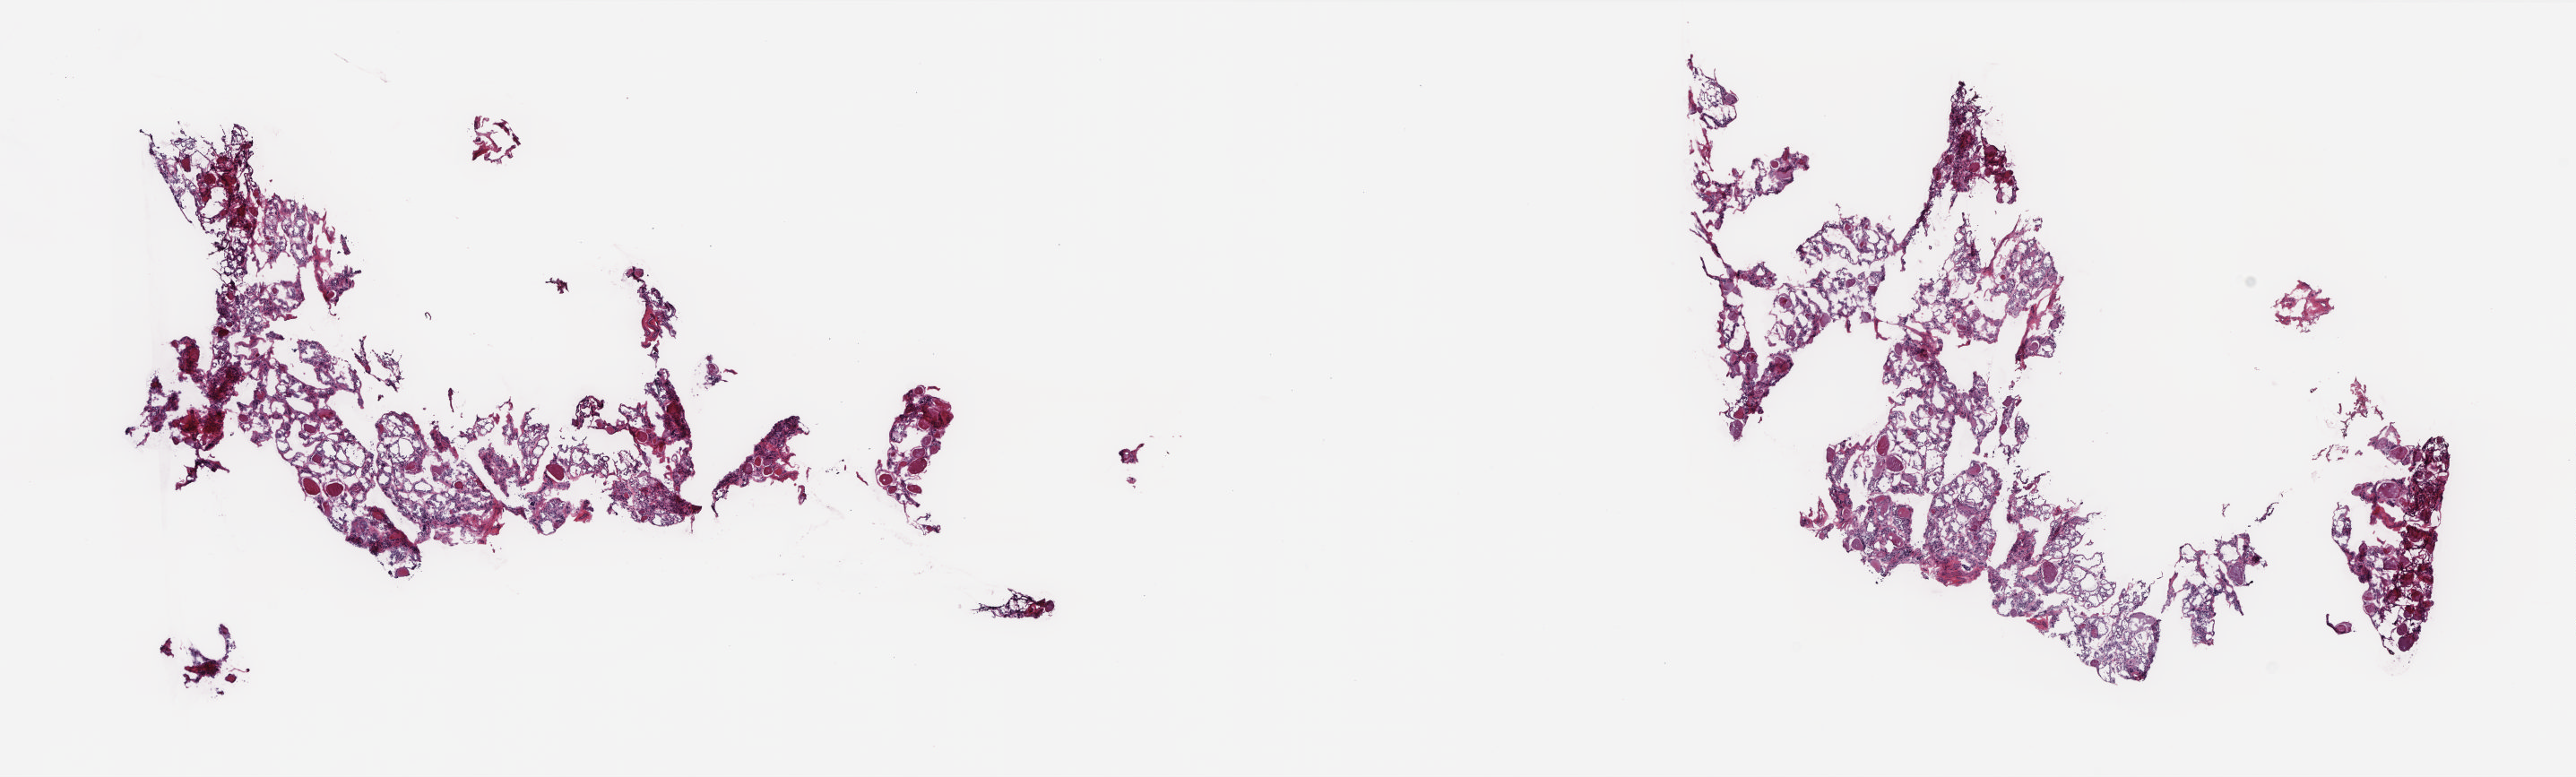
Whole-slide histology image, H&E, whole scanned area (about 23.0 x 6.9 mm, from a 20x scan) shown as a low-resolution overview, frozen section from the top of the tissue portion, sample: solid tissue normal (non-tumour tissue), thyroid. Patient: female, age at initial diagnosis 55 years. Pathologist review of this section (percent, as recorded): tumour cells 0%, tumour nuclei 0%, normal cells 100%, stromal cells 0%, necrosis 0%. Infiltration values recorded for this section: lymphocyte infiltration 4%, monocyte infiltration 1%, neutrophil infiltration 0%.
- this section: solid tissue normal (non-tumour) sample from the same patient
- patient diagnosis: Papillary adenocarcinoma, NOS (thyroid gland)